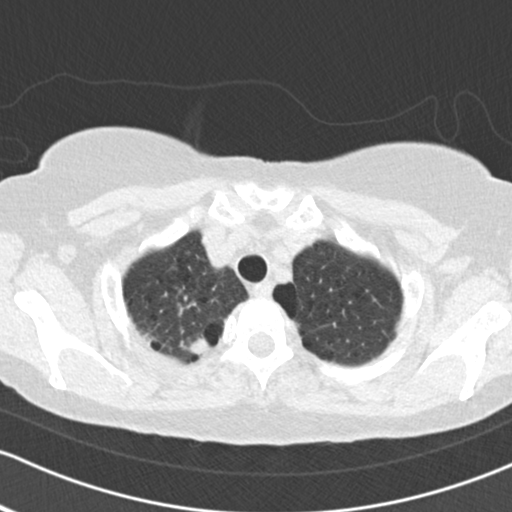
Low-dose screening chest CT, one axial slice; slice 145 of 161 in the series (ordered by position); lung window (W 1500 / L -600 HU); 2 mm slice thickness; 512 × 512 image matrix, field of view 312 × 312 mm.
Structures marked on this image (expert manual segmentation):
- lesion 1 (tumor, upper lobe of right lung): box from (x=185, y=335) to (x=211, y=356) px